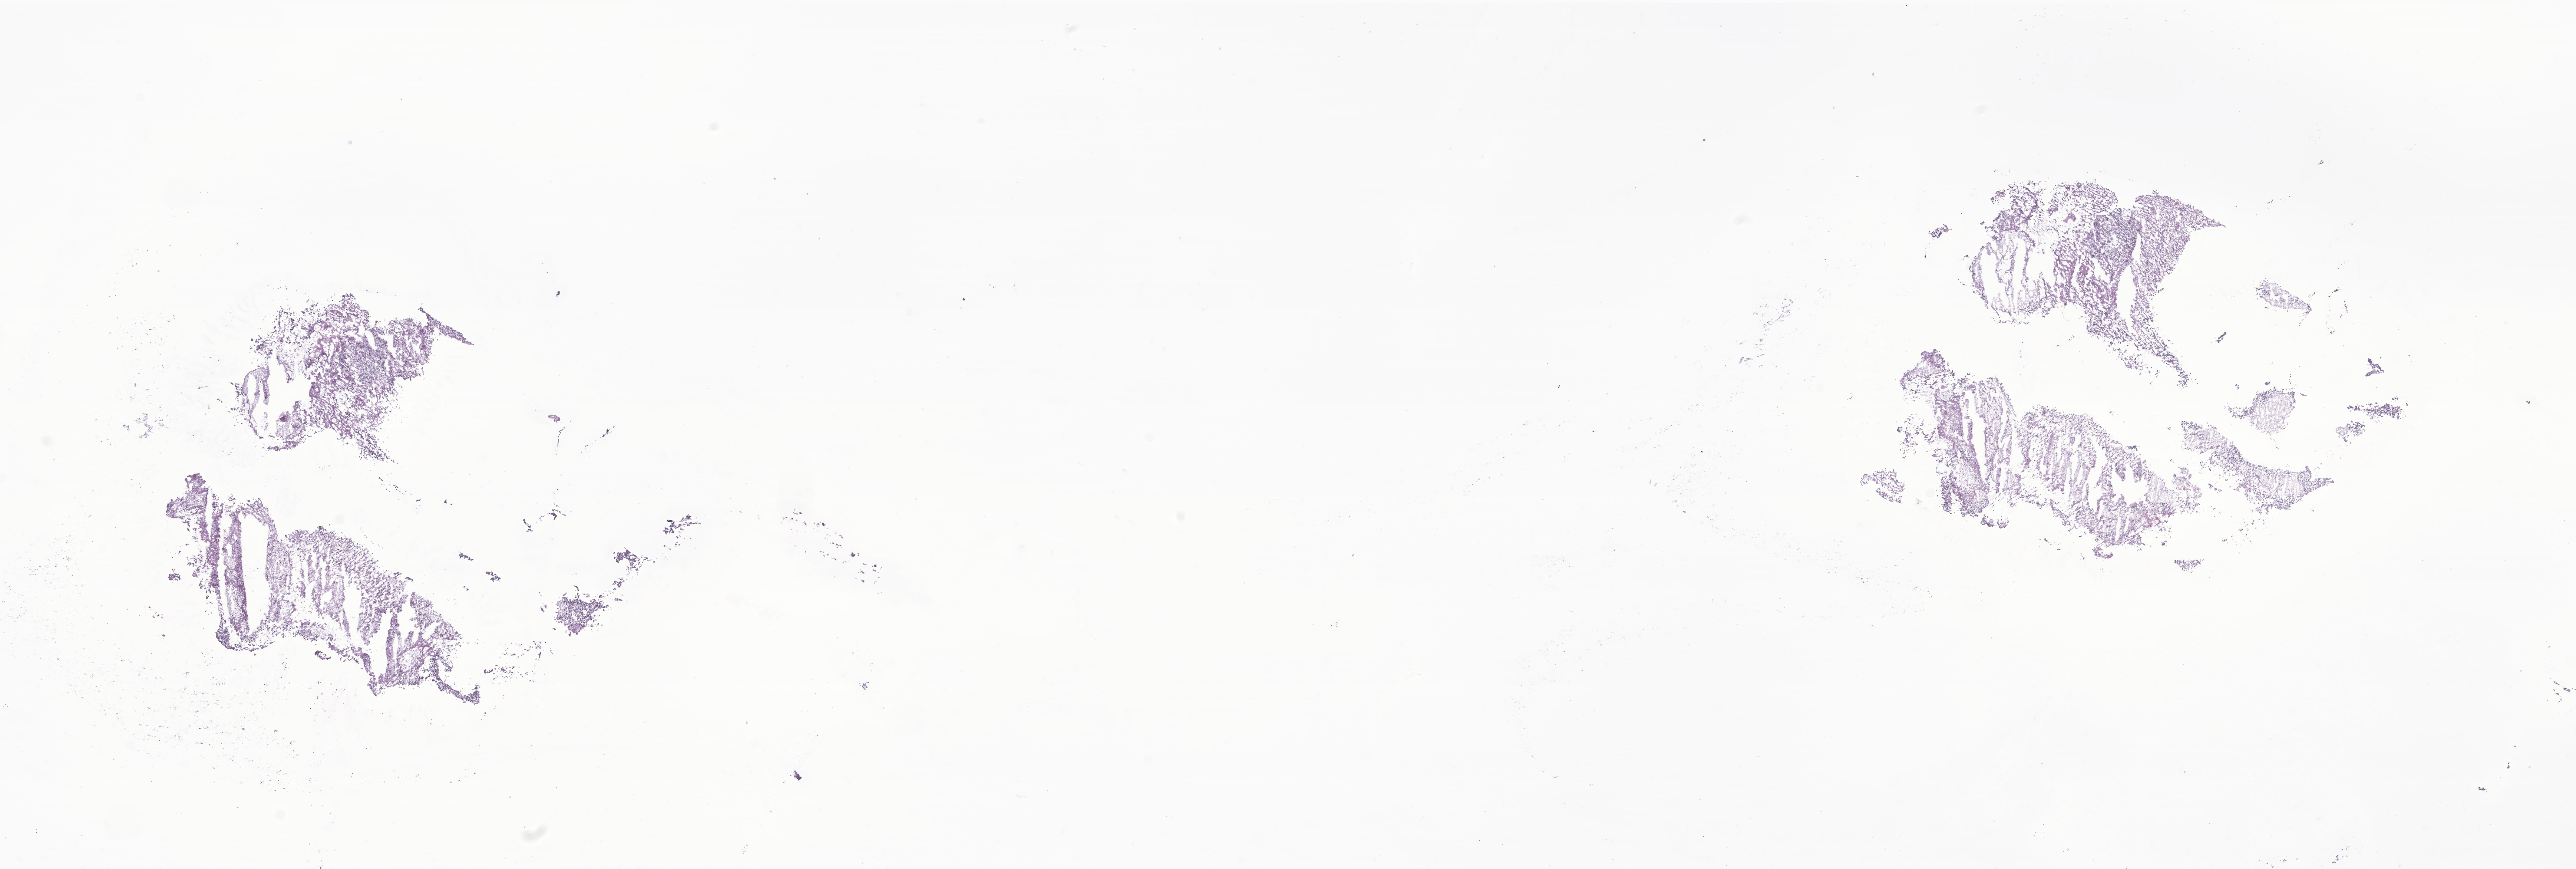
Whole-slide image, H&E stain of tumor tissue from the brain, low-resolution overview of the scanned area, about 29.3 x 9.9 mm, cryosection (OCT / tissue freezing medium). Female patient, age 197 months (16 years 5 months).
Recorded diagnosis: Neoplasm, malignant.